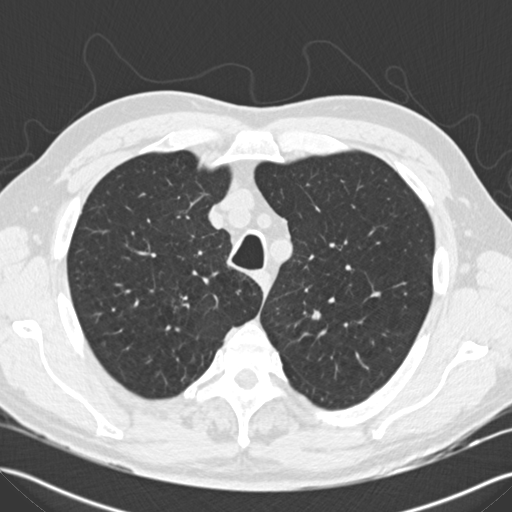
Low-dose screening chest CT, axial slice, baseline annual screen, lung window (W 1500 / L -600 HU), 2 mm slice thickness, standard (soft-tissue) reconstruction kernel (B30f), 120 kVp, slice 42 of 197 in the series, 512 × 512 image matrix, field of view 350 × 350 mm. Male participant, aged 66 years at enrolment. Current smoker at enrolment.
Expert reader's lesion annotation, bounding box (x1, y1, x2, y2) in pixels: (292, 299, 336, 339). Screening reader's record for this exam: no non-calcified nodule ≥4 mm recorded. Official screen result: negative screen, minor abnormalities not suspicious for lung cancer. Lung cancer was diagnosed 679 days after this screen (after the third annual screen): squamous cell carcinoma, NOS, left upper lobe, poorly differentiated (G3), stage IA (AJCC 6th edition), 15 mm at pathology.